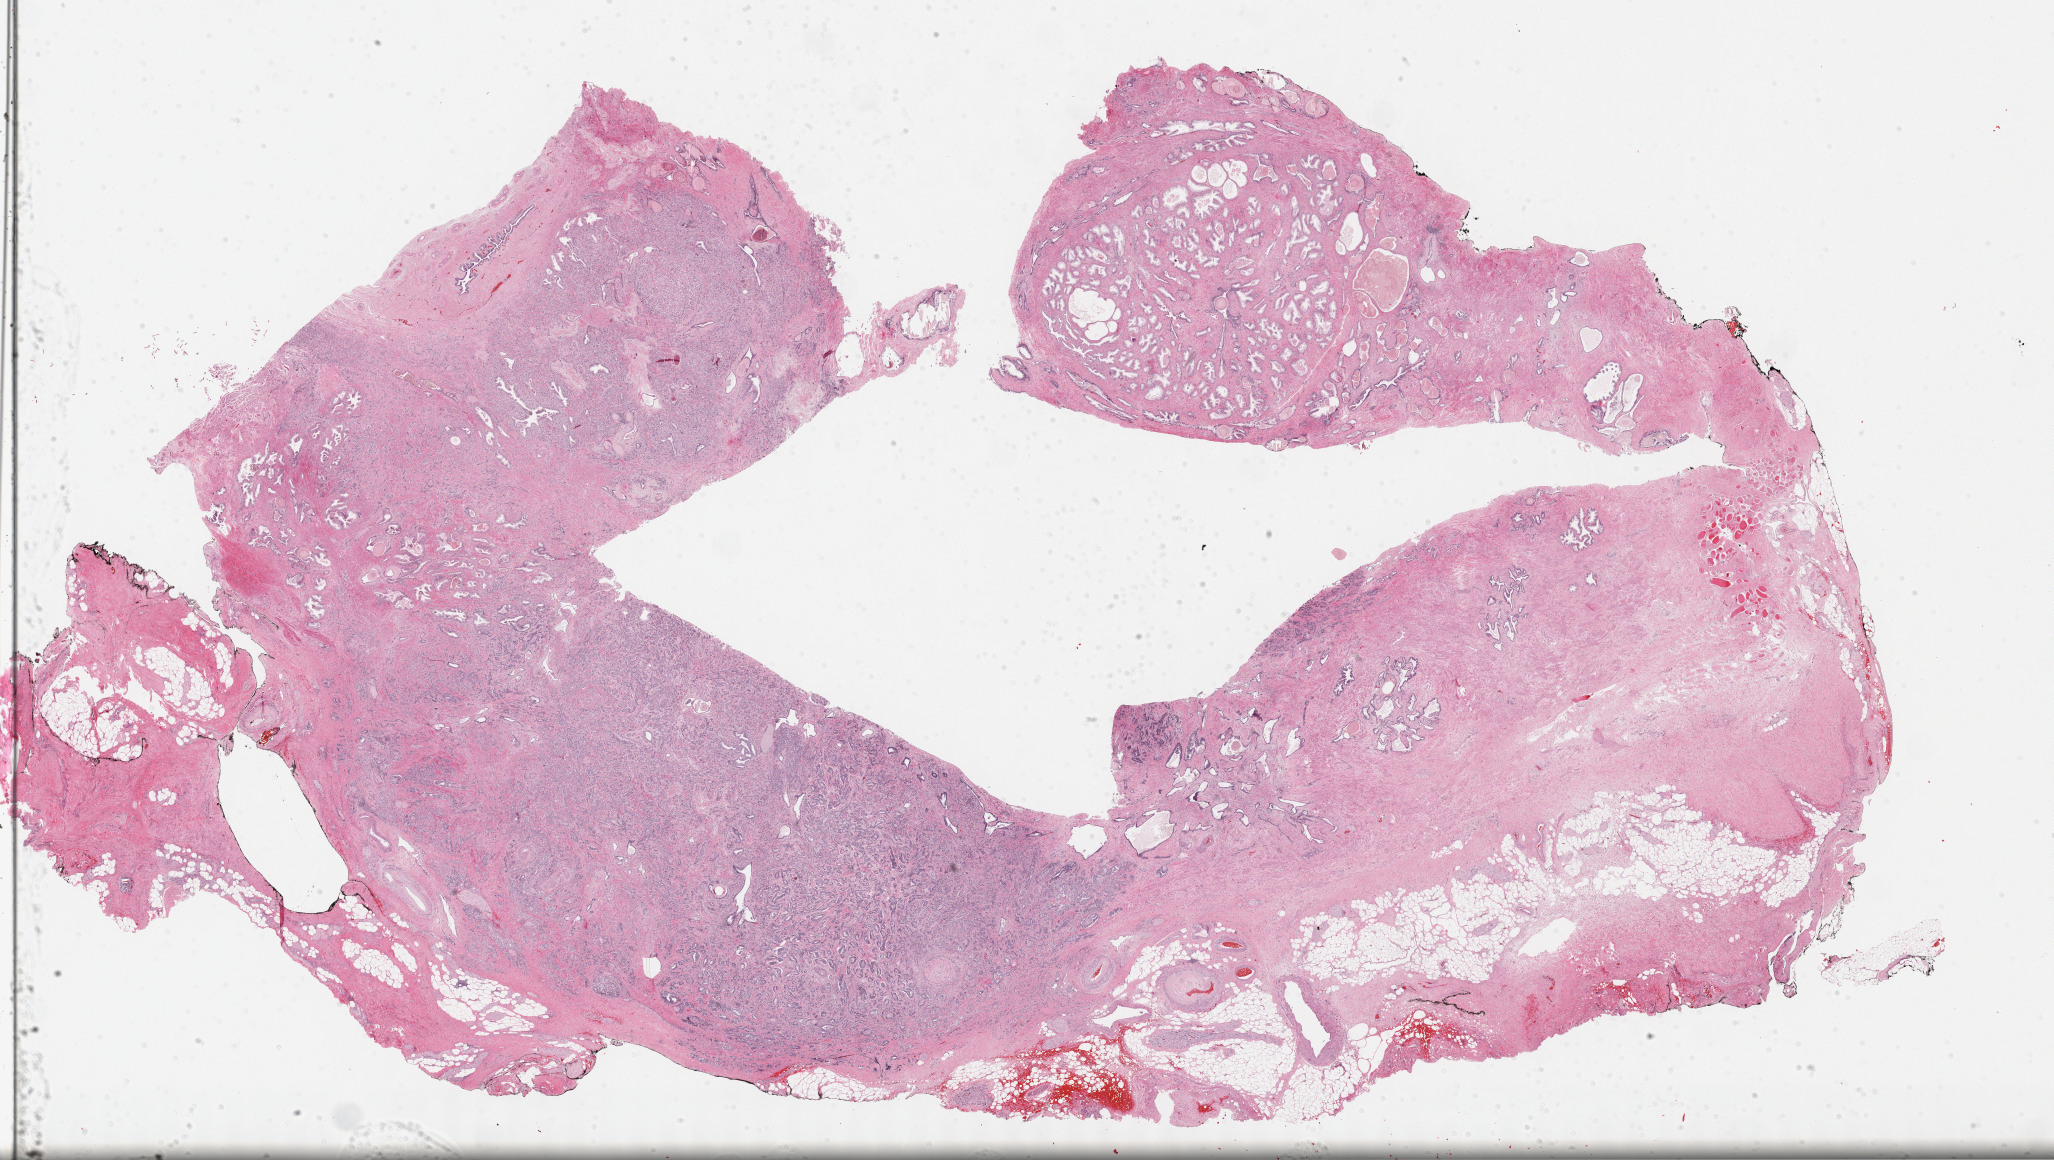
Whole-slide histology image, H&E, a low-resolution overview of the entire scanned area, about 33.2 x 18.8 mm (slide scanned at 40x); FFPE section; primary tumour sample from the prostate. Male, age 65 years at initial diagnosis.
Histologic diagnosis: Adenocarcinoma, NOS.